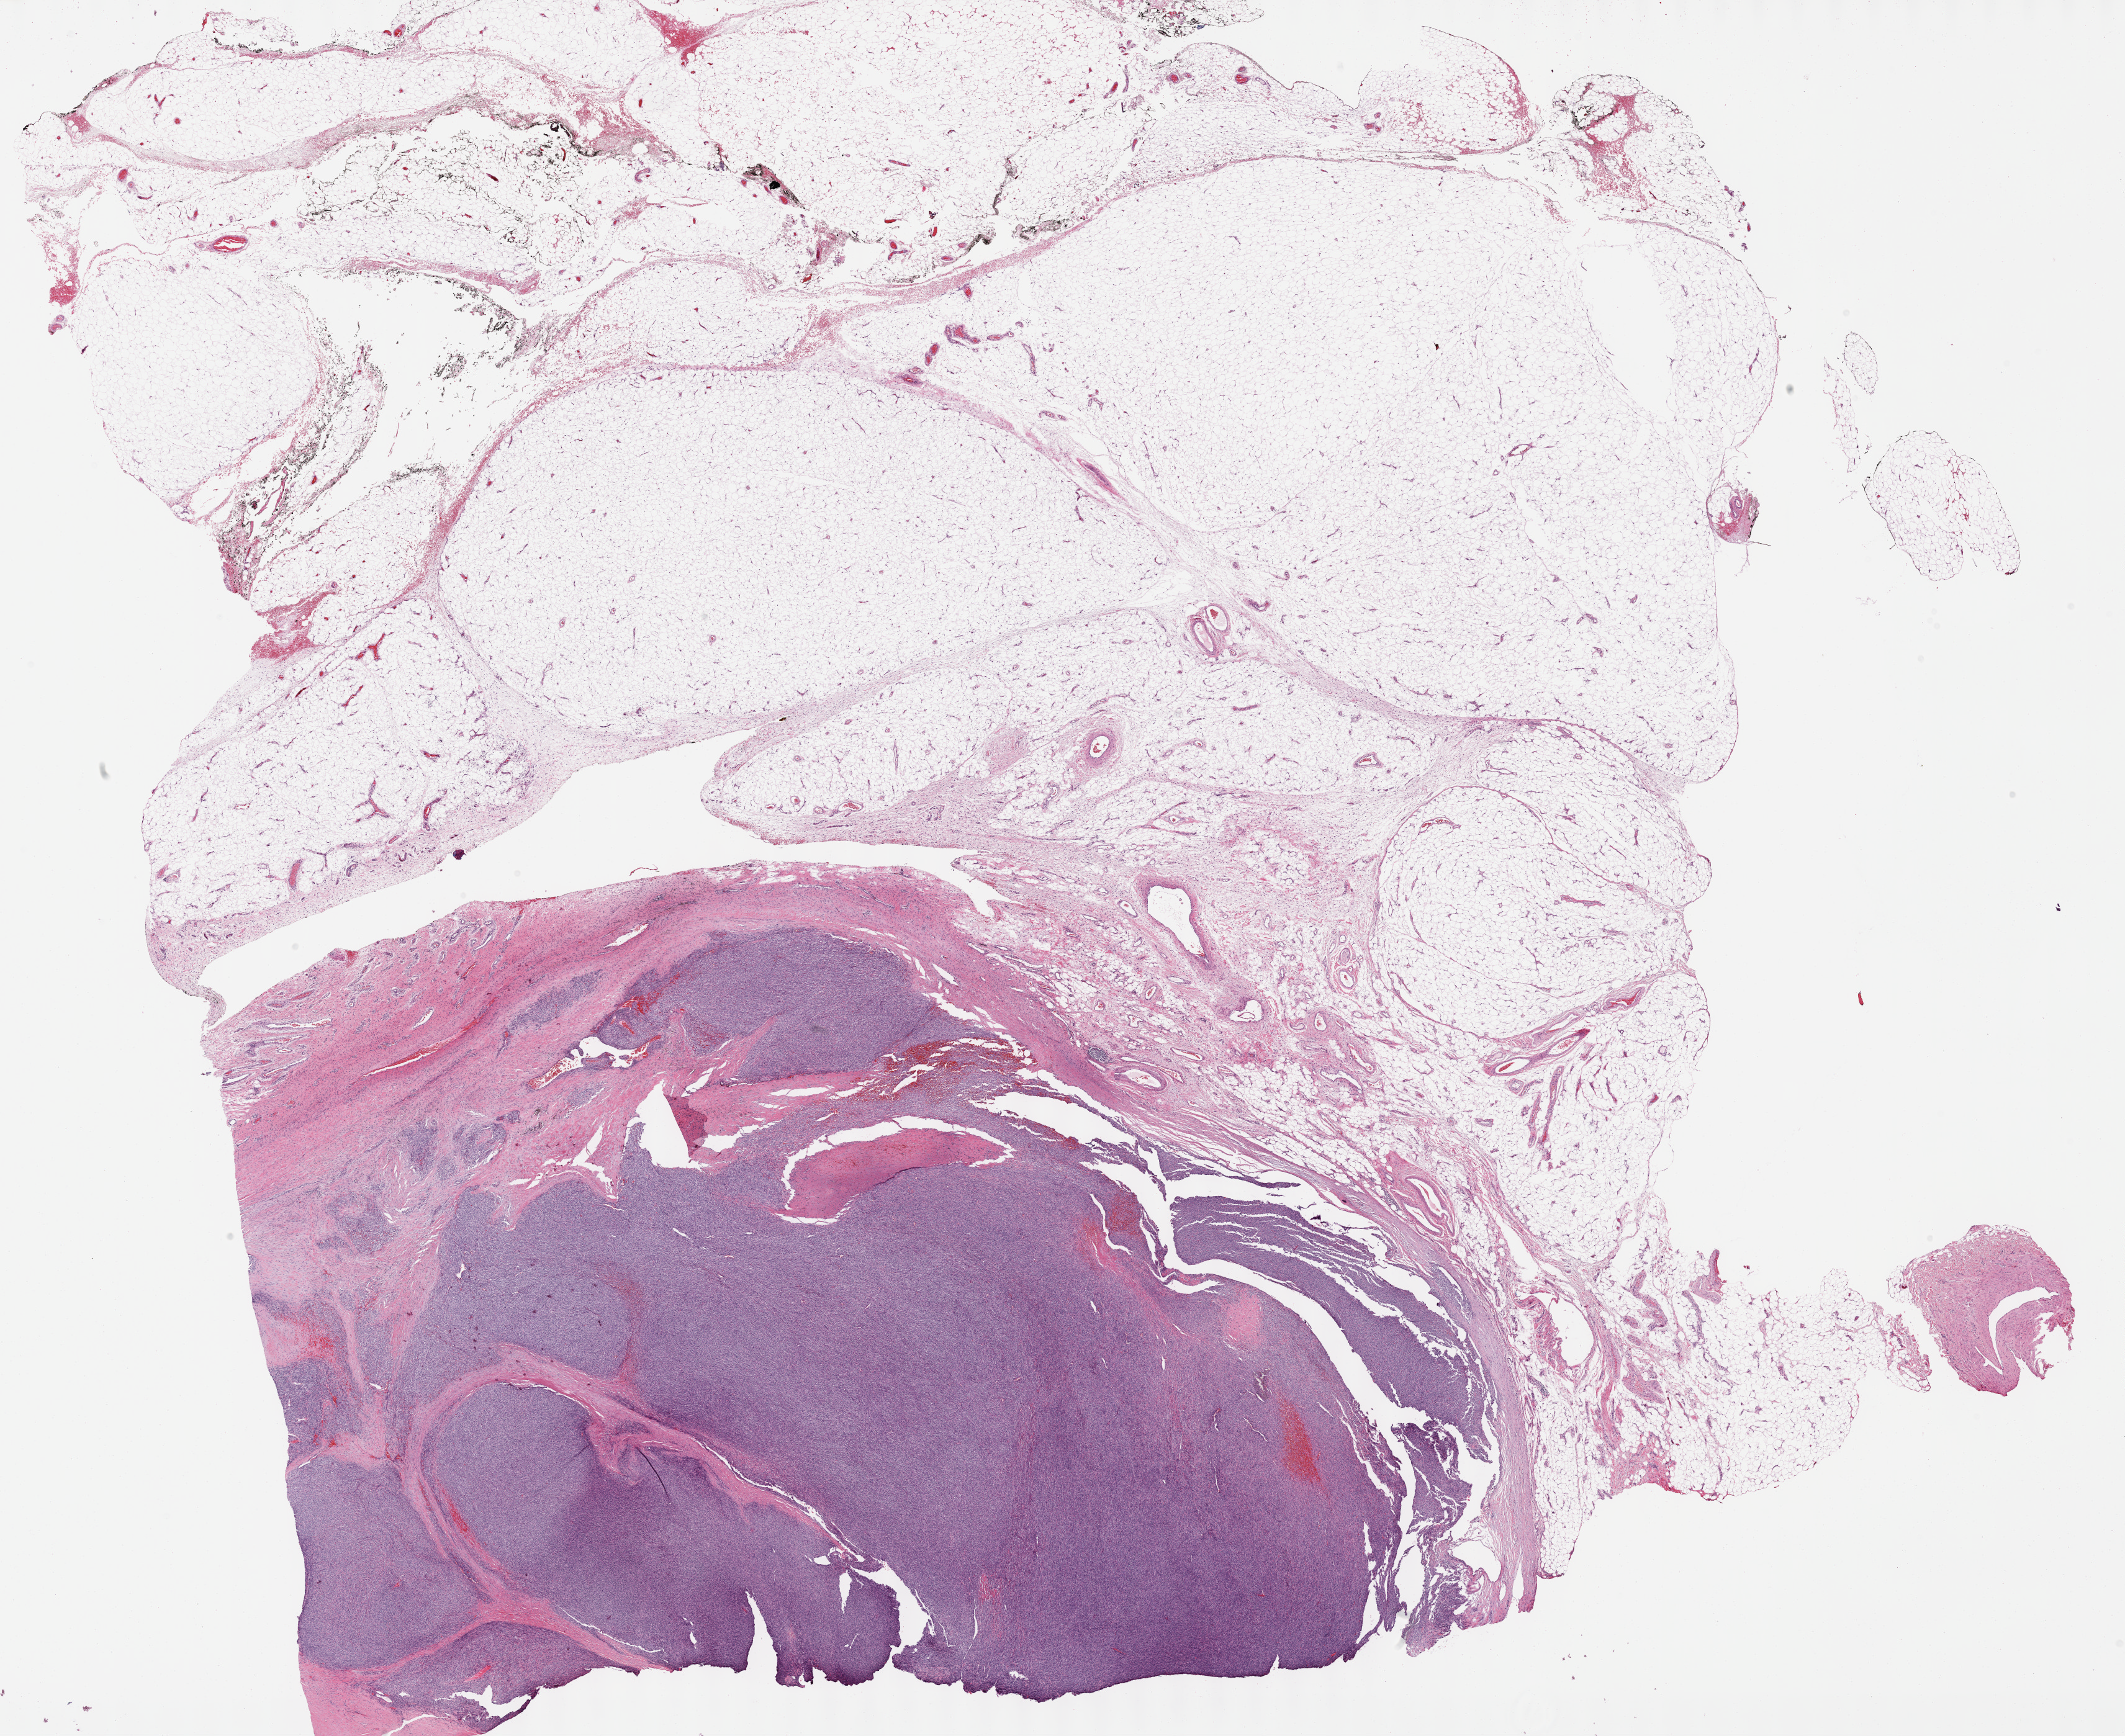
Digitized H&E tissue section (whole slide) — a low-resolution overview of the entire scanned area, about 27.7 x 22.6 mm; formalin-fixed paraffin-embedded (FFPE) diagnostic section; sample: primary tumour, connective, subcutaneous and other soft tissues. Male, age 72 years at initial diagnosis.
- pathologic diagnosis: Synovial sarcoma, spindle cell